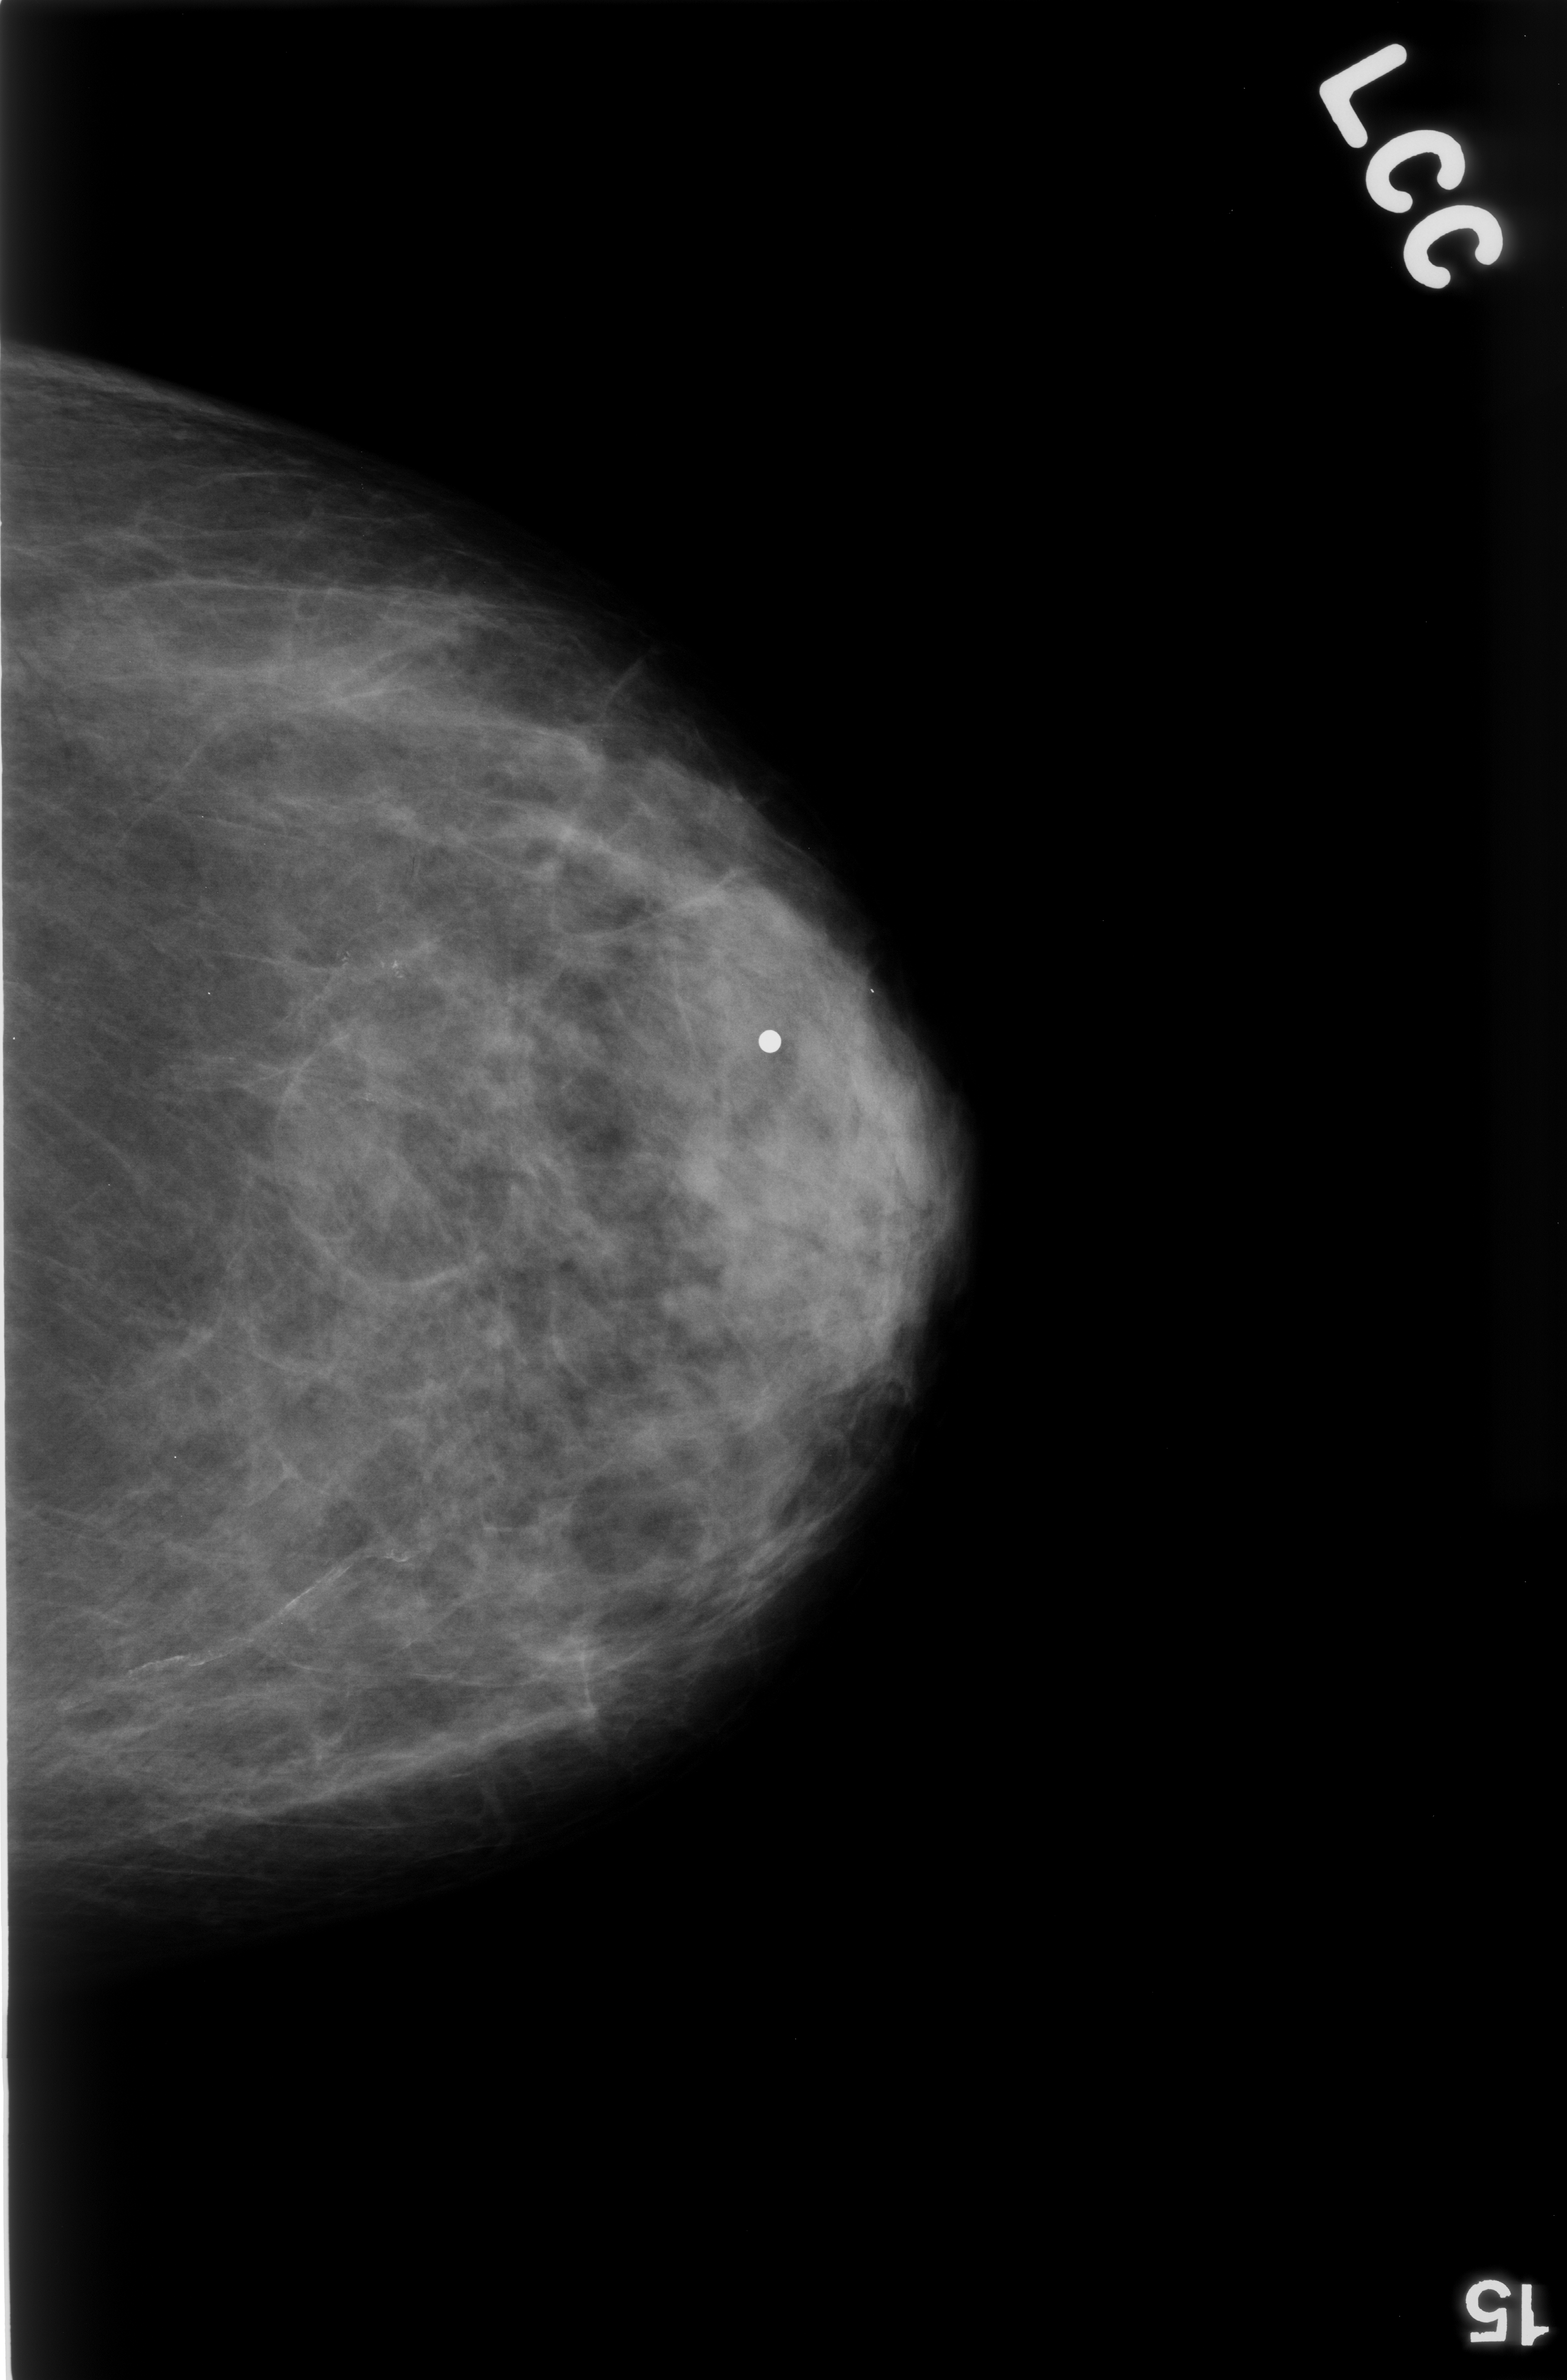
Digitized screen-film mammogram, left breast, CC view, breast composition: scattered fibroglandular densities (BI-RADS density category 2 of 4).
Finding: calcifications, morphology pleomorphic, distribution clustered; BI-RADS assessment category 4; pathology result (as recorded, not read from the image): benign.